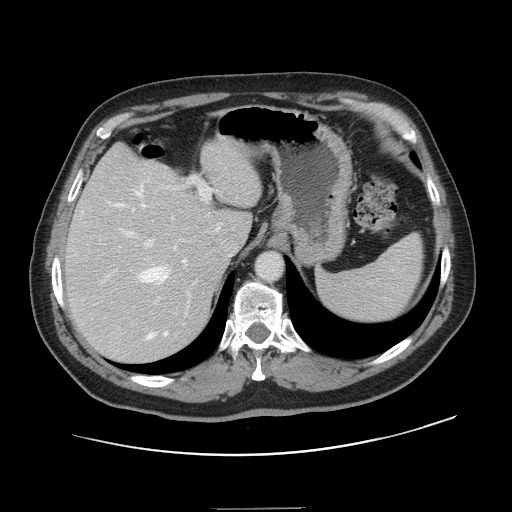
Contrast-enhanced abdominal CT, one axial slice. Position 103 of 143 along the scan axis. 120 kVp. Intravenous contrast given. Soft-tissue window (W 400 / L 40 HU). 2.5 mm slice thickness. 512 × 512 image matrix, field of view 402 × 402 mm. Male patient, age 62 years. Case-level facts recorded for this patient, not image findings: diagnosis: colorectal cancer liver metastases, imaged before liver resection; multiple liver metastases: yes; largest metastasis: 2.7 cm; disease in both lobes: no.
Outlined on this slice (expert manual segmentation):
- hepatic veins: box from (x=108, y=187) to (x=187, y=339) px
- liver: (x=67, y=141)–(x=261, y=362)
- planned liver remnant (the part of the liver to remain after resection): (x=67, y=140)–(x=261, y=267)
- portal vein (with intrahepatic branches): (x=103, y=177)–(x=212, y=333)